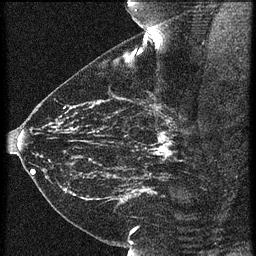
Breast MRI (dynamic contrast-enhanced), one sagittal slice. Position 39 of 60 along the scan axis. 3 images stored at this slice position (order not interpretable as contrast timing). 1.5 T. TE 4.2 ms, TR 21.3 ms. 256 × 256 image matrix. Female patient, age 43 years. From the clinical record (not read from this slice): setting: breast cancer imaged before/during neoadjuvant chemotherapy; receptor status: HER2-positive.
Outlined on this slice (semi-automatically segmented with operator editing):
- analysis volume of interest (the breast-tissue region the enhancement analysis was run in; not a lesion): box from (x=119, y=114) to (x=189, y=173) px
- tumour enhancement mask (voxels above the 90 % enhancement threshold inside the analysis volume of interest): (x=154, y=122)–(x=173, y=161)